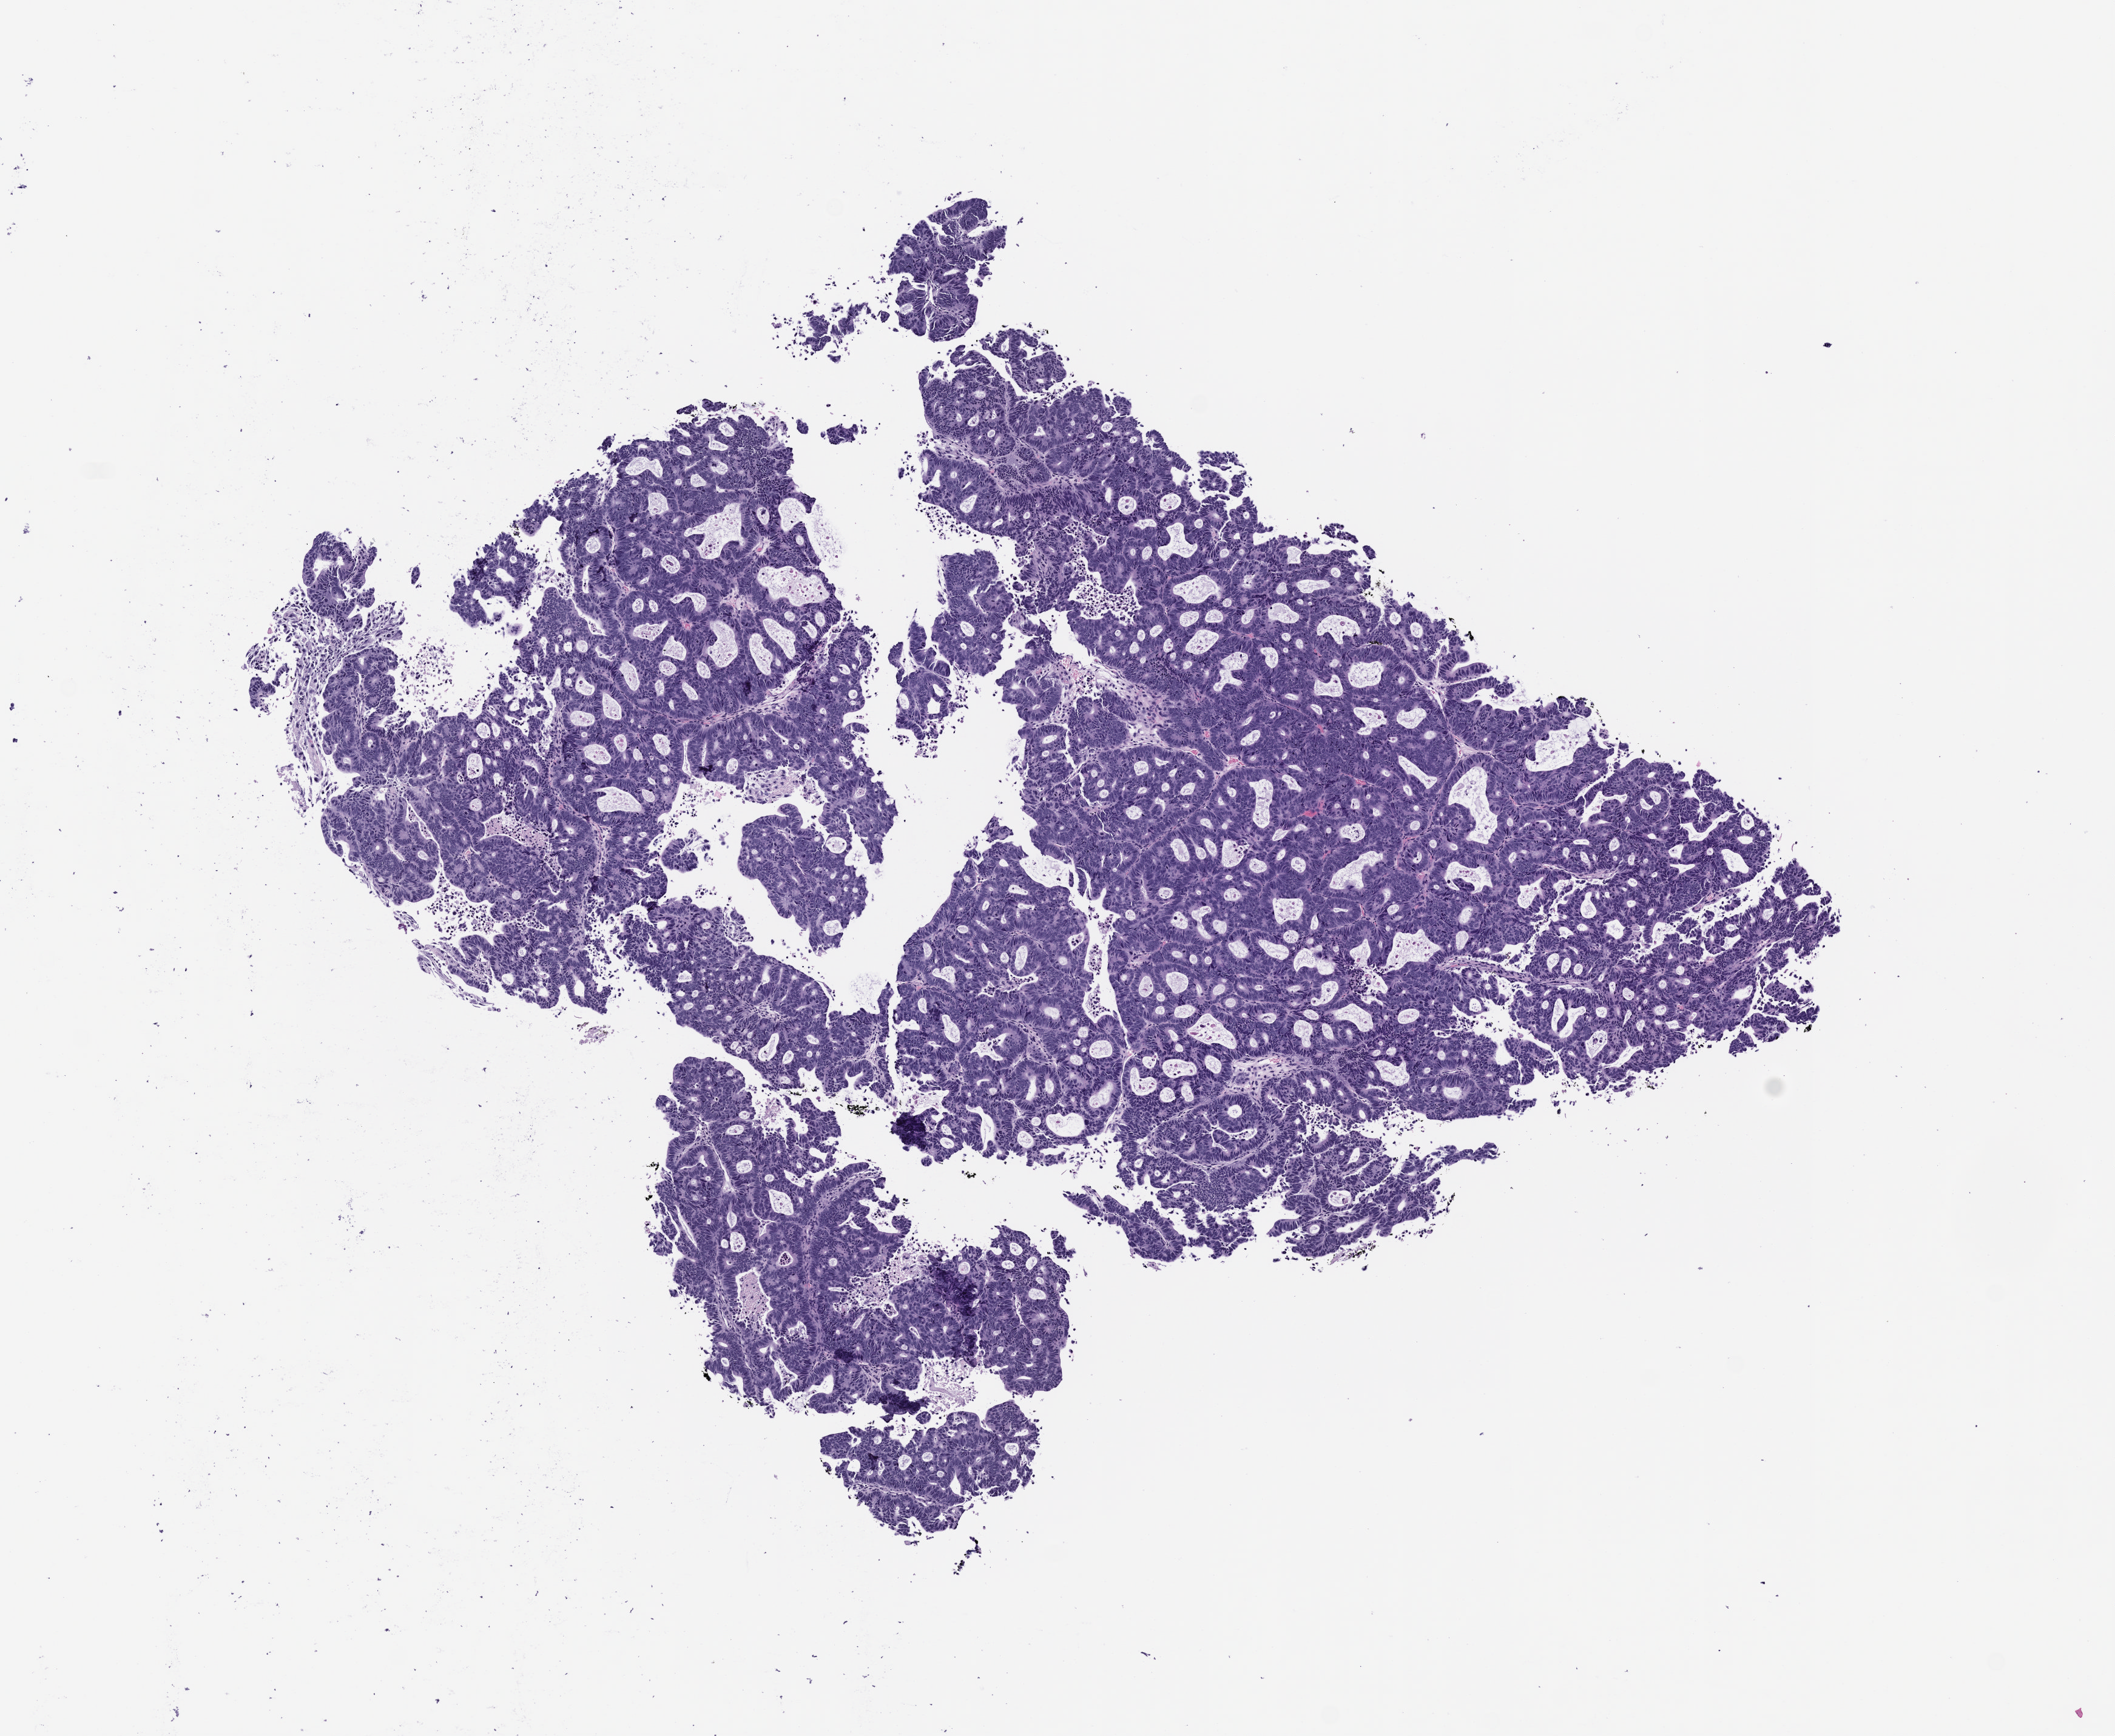
Haematoxylin and eosin whole-slide image of a patient-derived xenograft (PDX) tumor grown in a mouse, passage 2, low-resolution overview of the scanned area, about 7.0 x 5.8 mm. FFPE section. Originating tumor site category: rectum.
- originating patient diagnosis: Rectal Adenocarcinoma